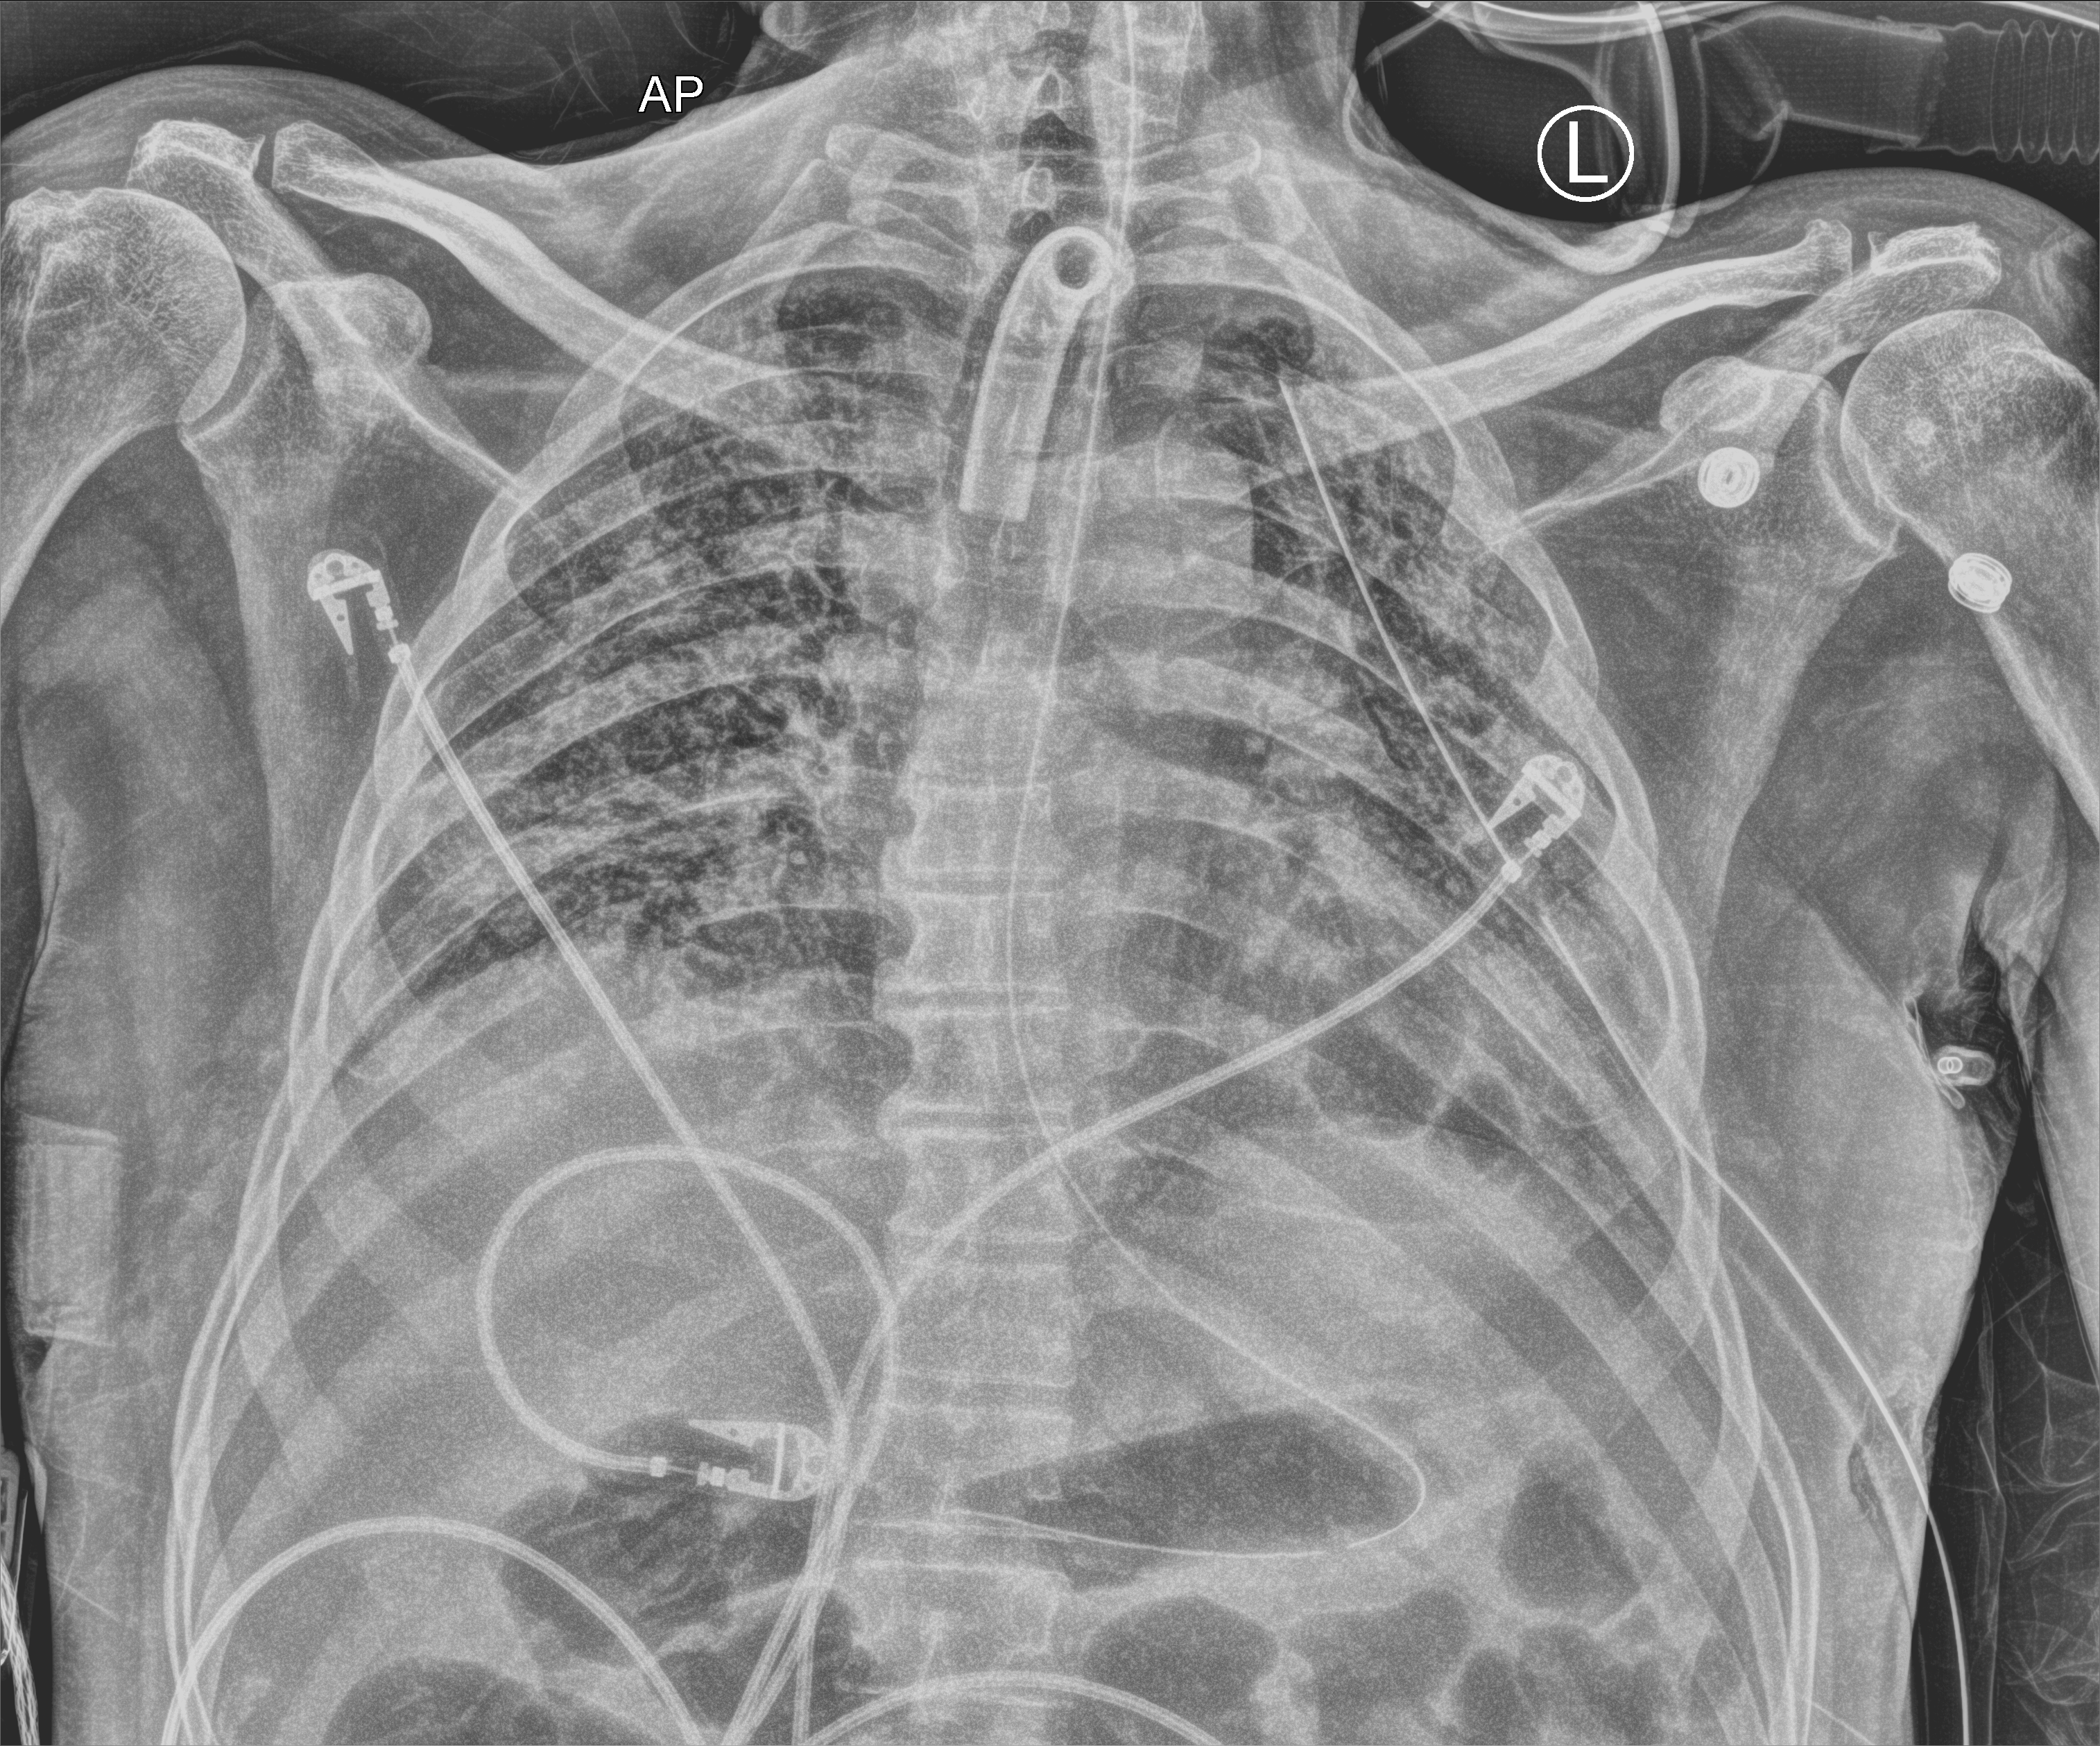
Bedside chest radiograph (computed radiography); anteroposterior (AP) projection. Patient hospitalised with COVID-19; male, aged 18–59 years.
Hospital-stay facts (about this admission, not read from this image; timing relative to this image not recorded): admitted to intensive care during this hospital stay: yes.